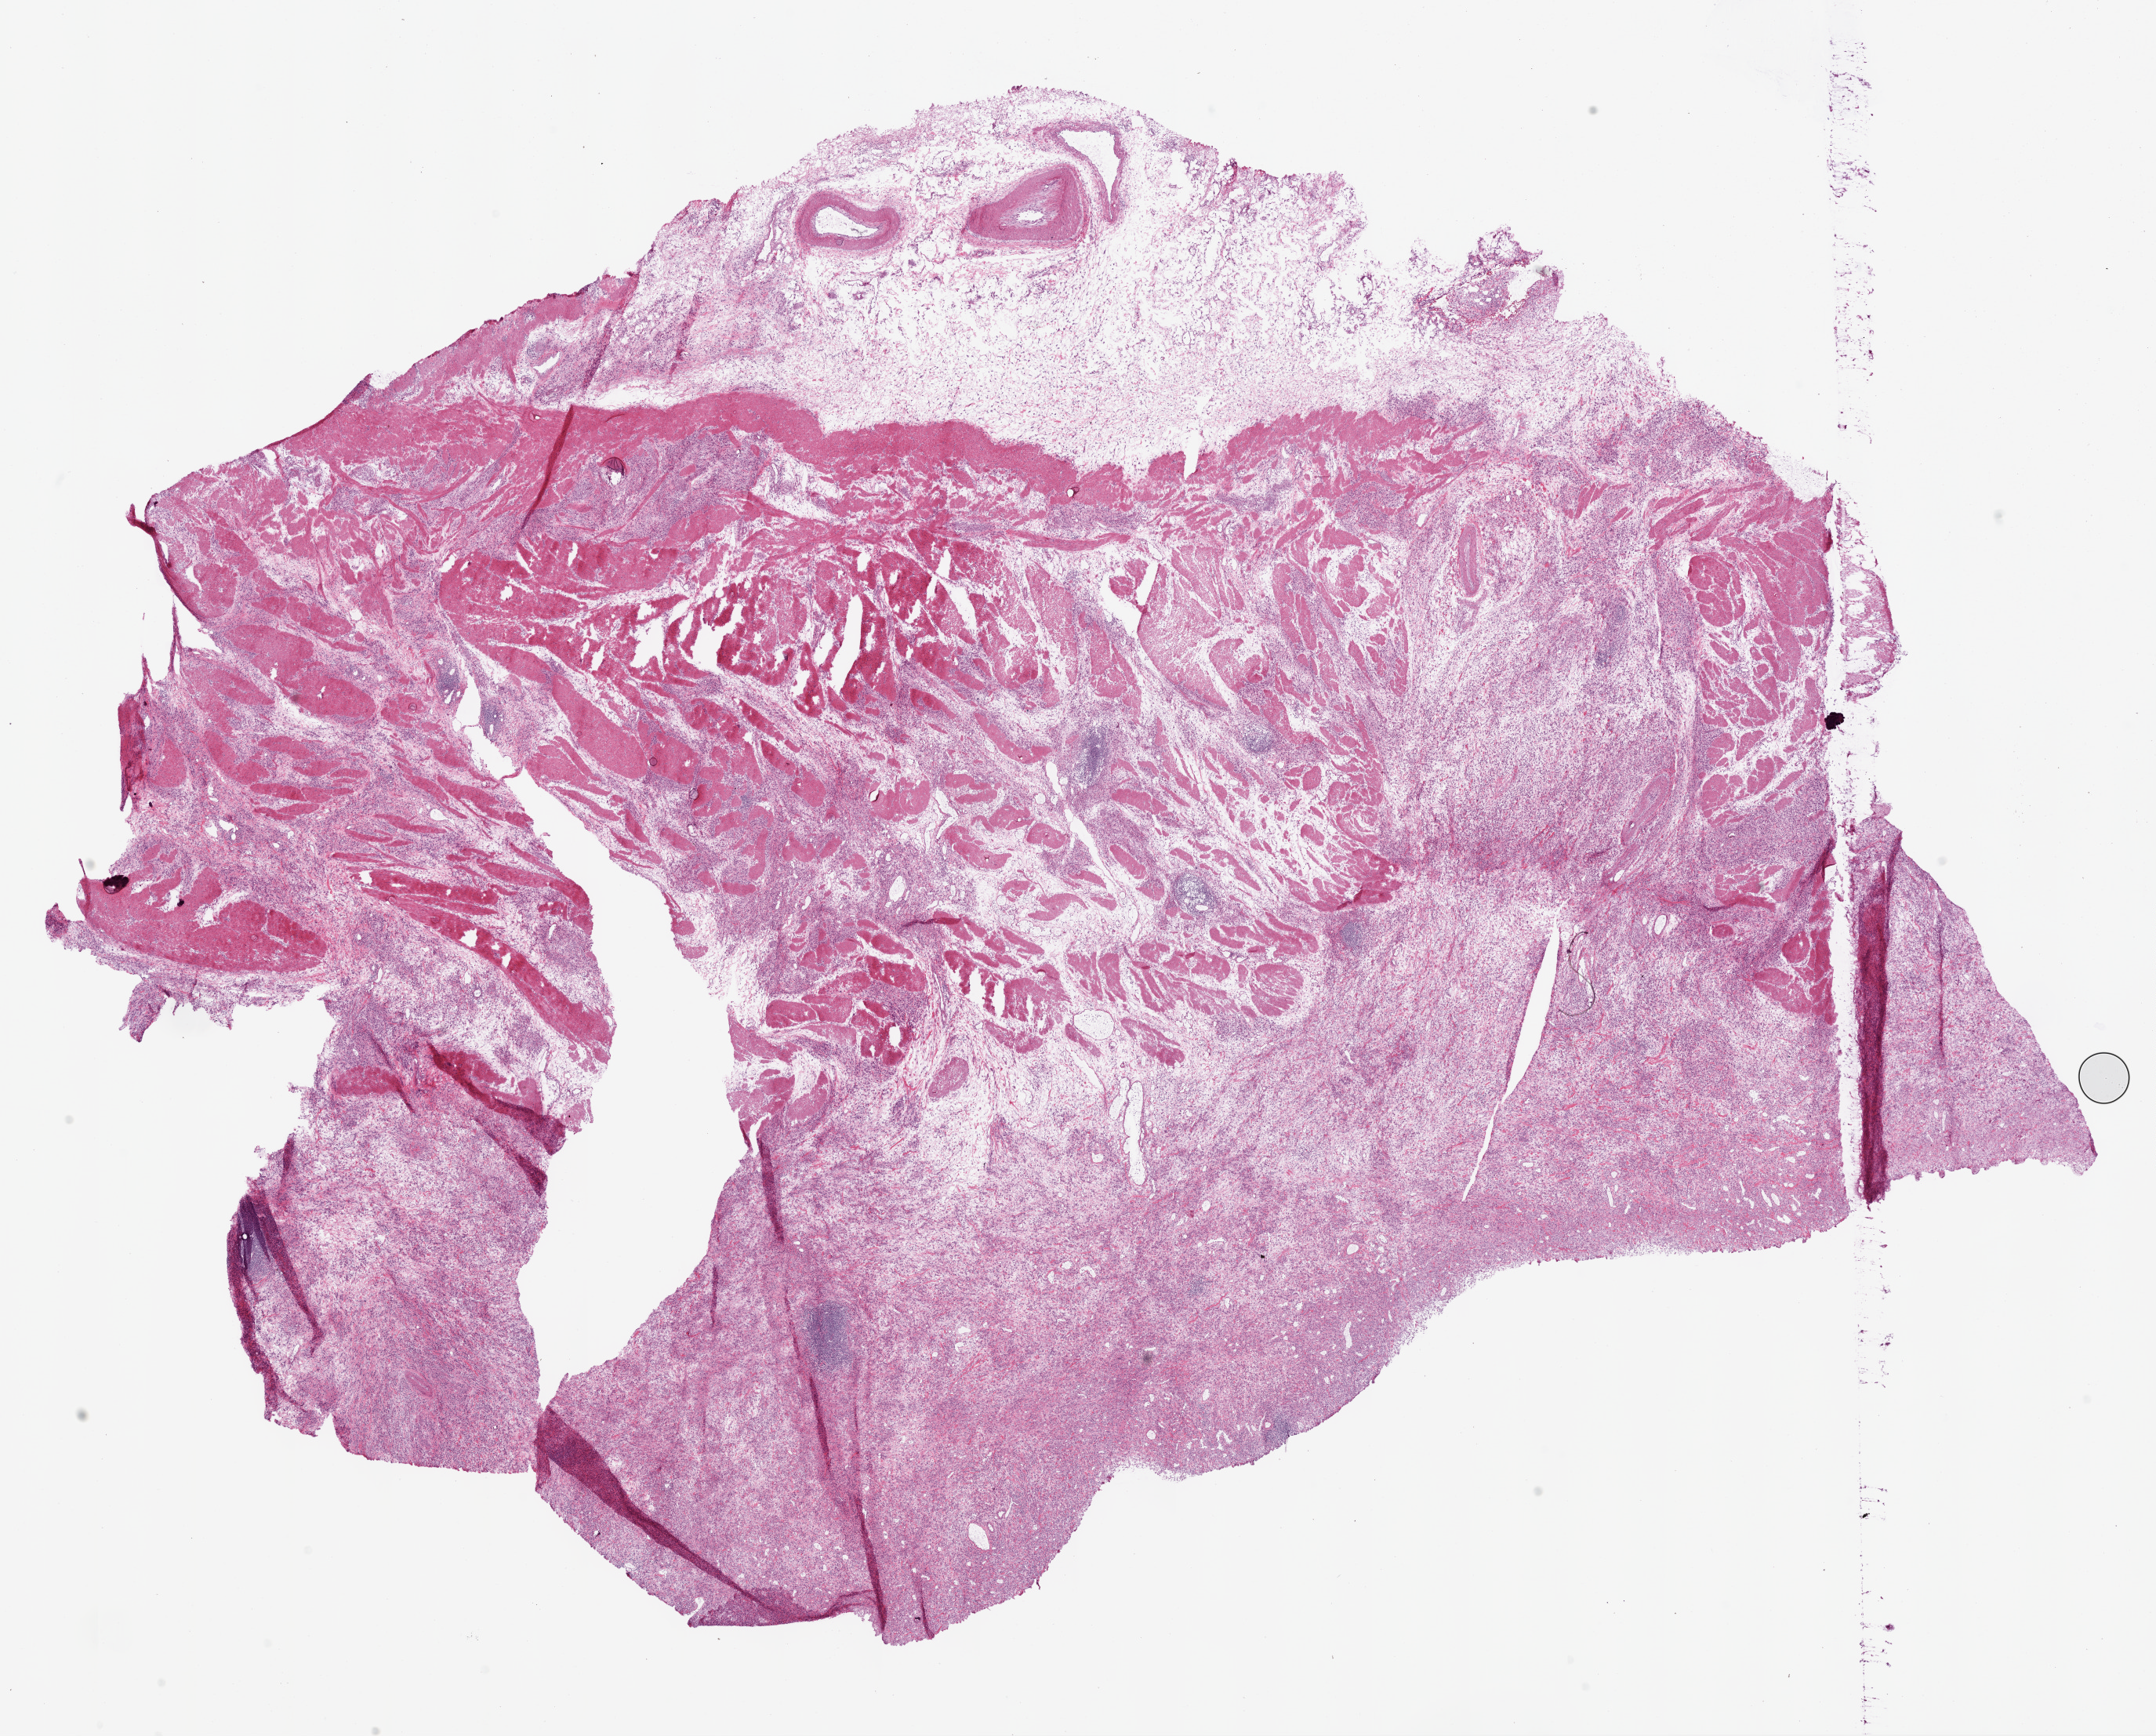
Whole-slide histology image, H&E — shown as a low-resolution overview of the whole scanned area (about 22.1 x 17.8 mm, from a 20x scan), frozen section from the bottom of the tissue portion, primary tumour sample from the stomach. Male, age 56 years at initial diagnosis. Histologic grade: G3 (poorly differentiated). Pathologist review of this section (percent, as recorded): tumour cells 70%, tumour nuclei 80%, normal cells 10%, stromal cells 20%, necrosis 0%.
Histologic diagnosis: Adenocarcinoma, NOS (gastric antrum).